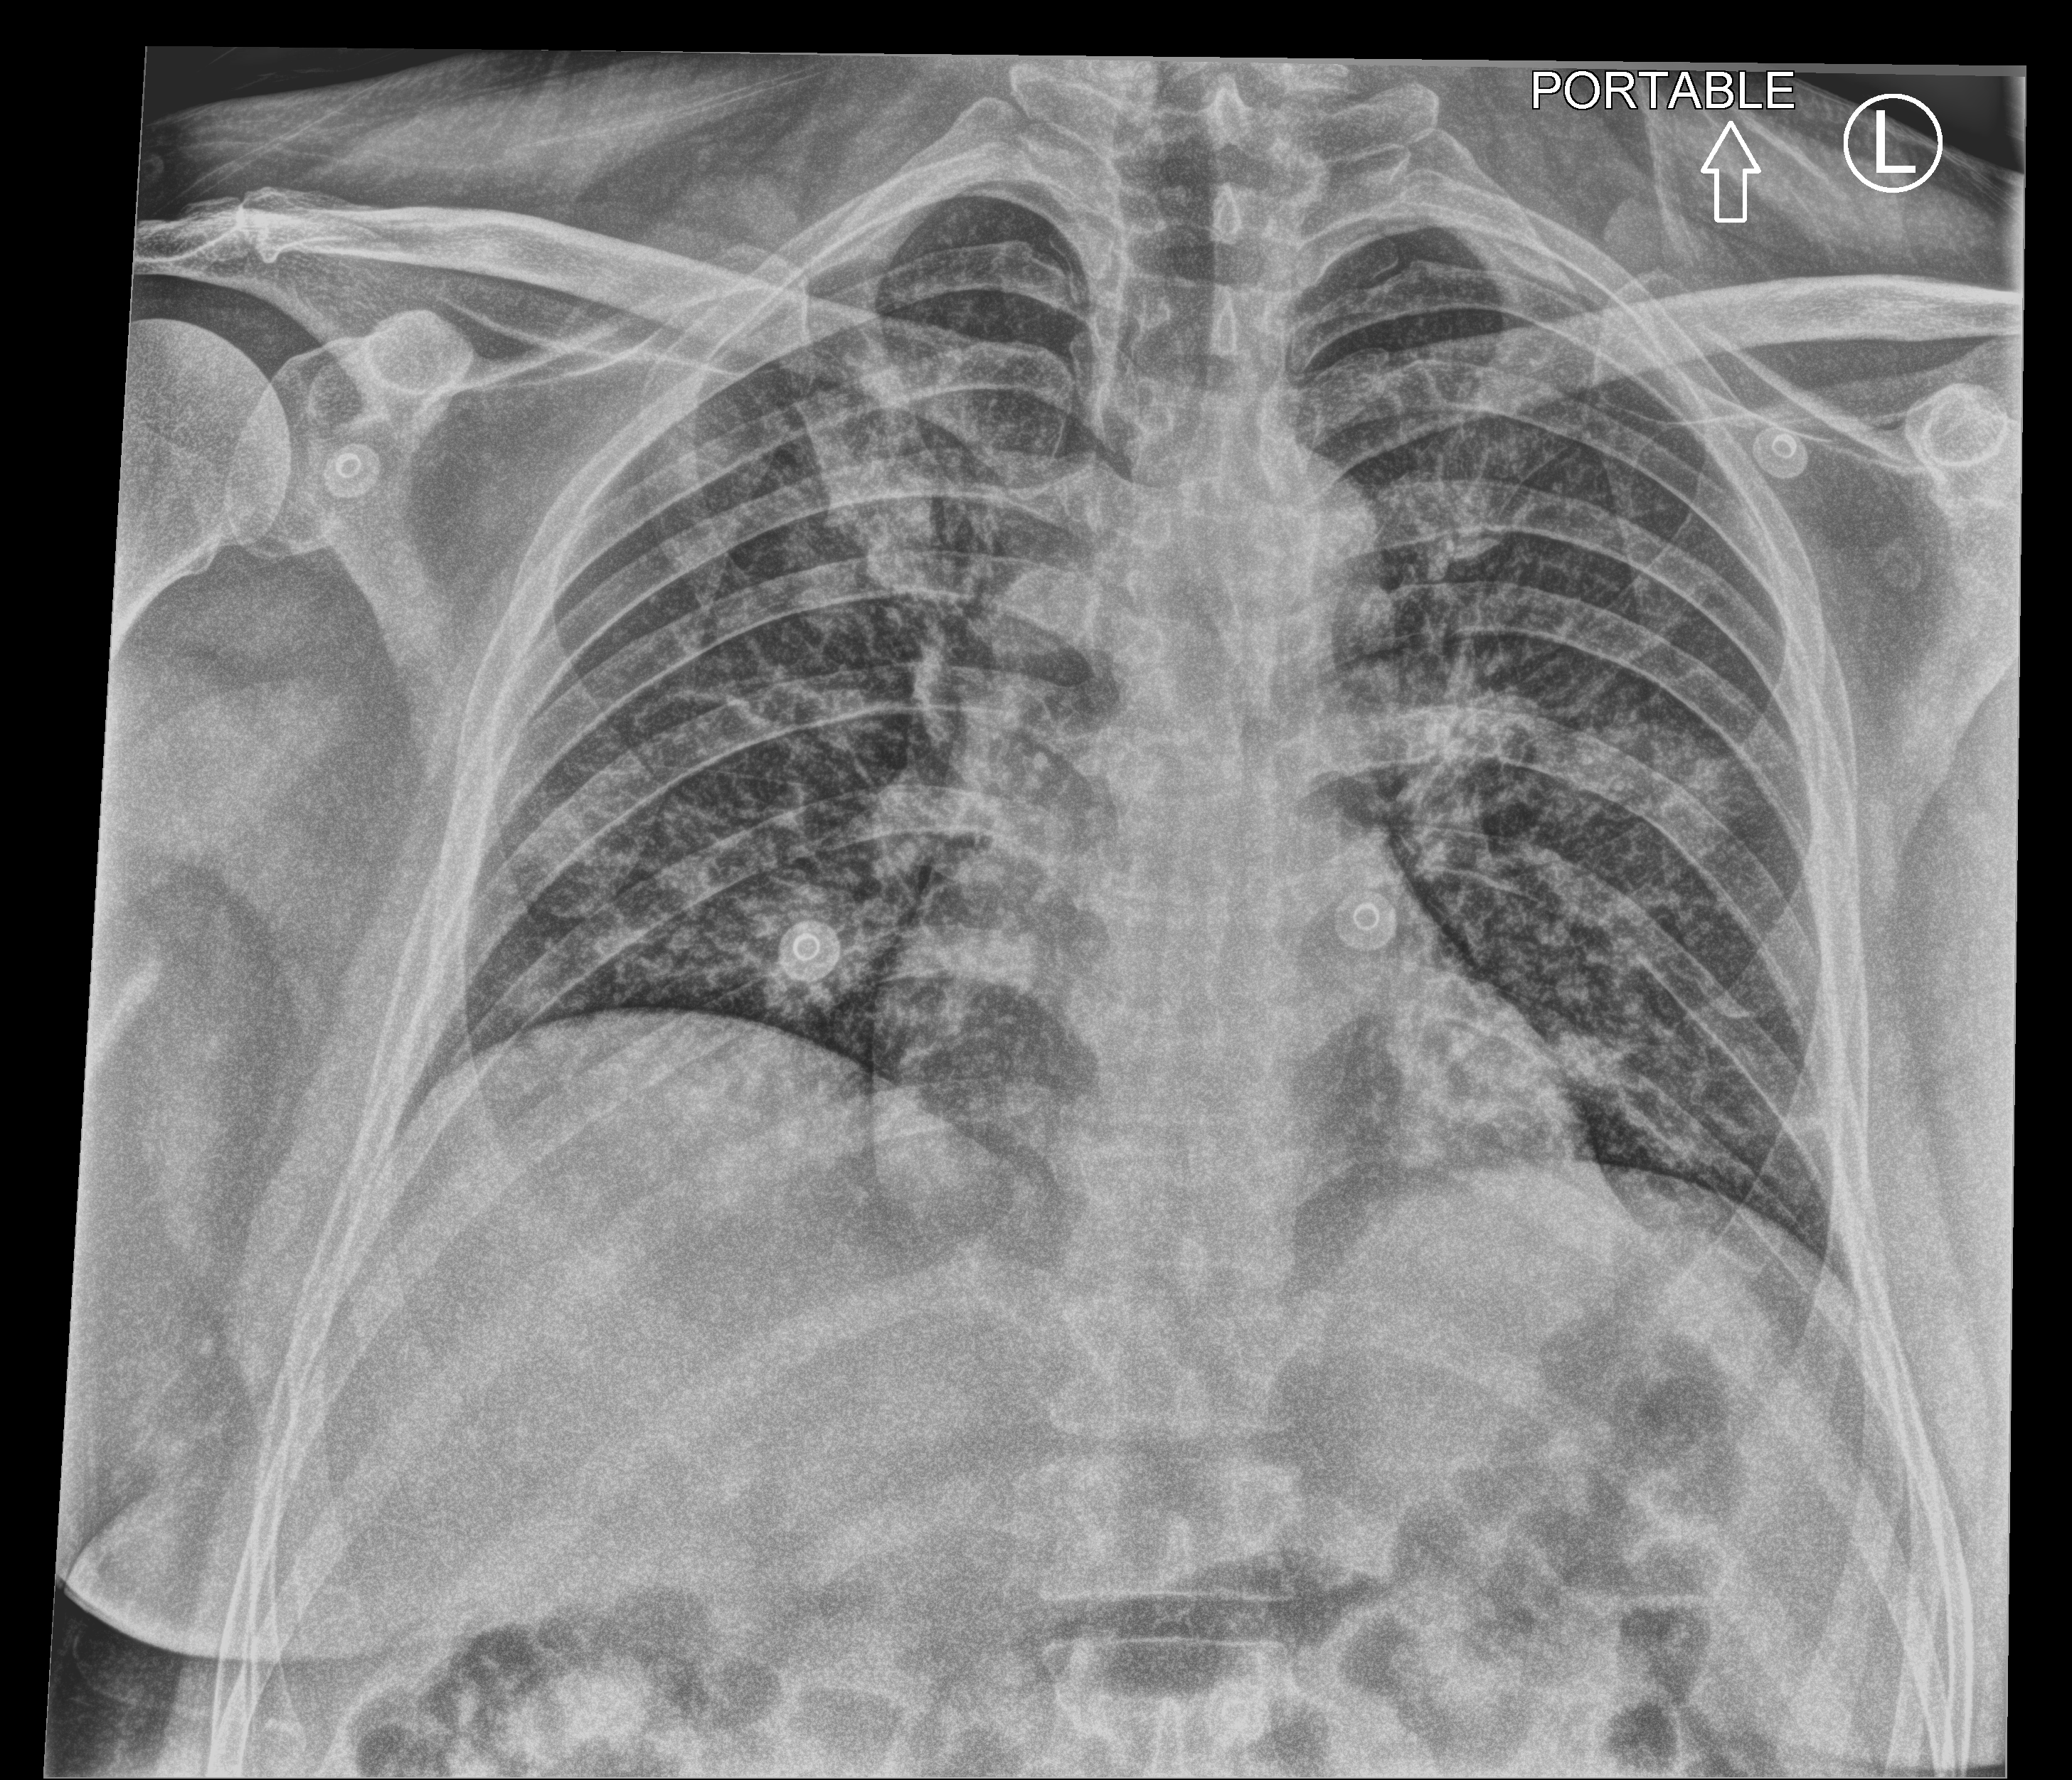
Portable chest radiograph; anteroposterior (AP) projection. Male patient hospitalised with COVID-19, age 18–59 years.
Admission-level facts for this patient (not findings on this image; timing relative to this image not recorded): mechanically ventilated during this hospital stay: no; admitted to intensive care during this hospital stay: no.